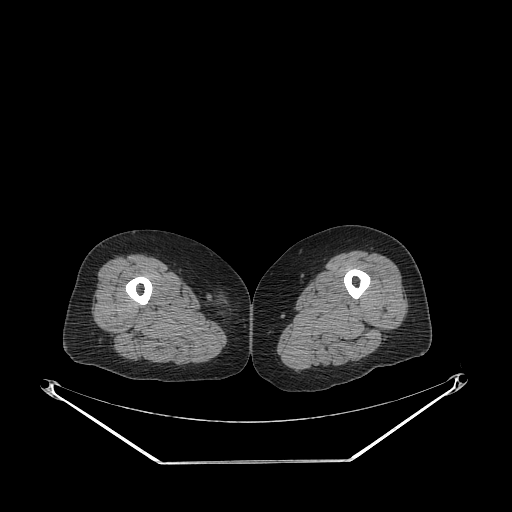
CT of an extremity soft-tissue mass (from a PET/CT study), one axial slice; slice 226 of 311 in the series (ordered by position); reconstruction kernel STANDARD; 140 kVp; soft-tissue window (W 400 / L 40 HU); 512 × 512 image matrix, field of view 500 × 500 mm. Female patient. Case-level facts recorded for this patient, not image findings: histological type: leiomyosarcoma; grade: intermediate; site of the primary tumour: parascapusular.
Annotated regions visible in this slice (expert contour drawn on MRI and transferred to this co-registered scan by the dataset authors):
- gross tumour volume including surrounding oedema: bounding box (x1, y1, x2, y2) in pixels: (215, 301, 223, 307)